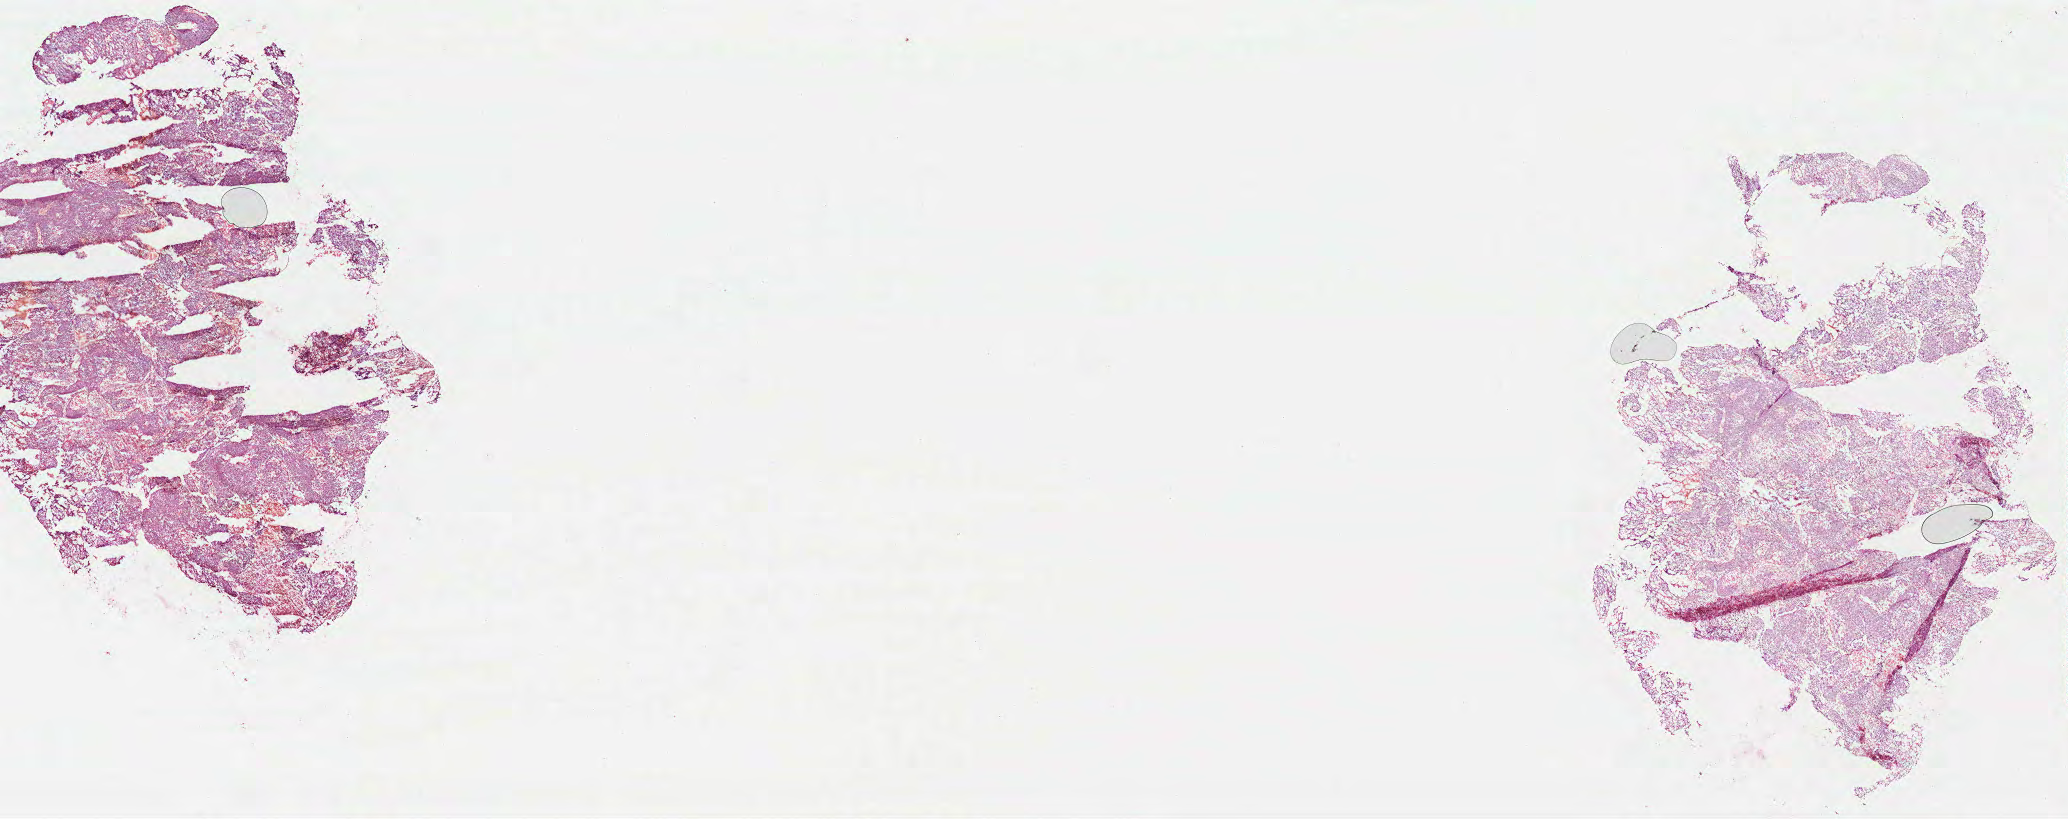
Whole-slide histology image, H&E-stained — low-resolution overview of the scanned area, about 33.4 x 13.2 mm, FFPE section, head and neck, primary tumour sample. Patient: male, age at initial diagnosis 73 years. Histologic grade: G3 (poorly differentiated).
- histologic diagnosis: Squamous cell carcinoma, NOS (base of tongue, NOS)